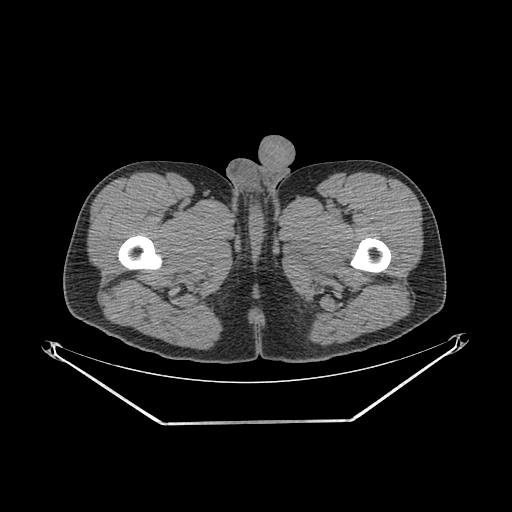
CT of an extremity soft-tissue mass (from a PET/CT study), one axial slice. Slice 266 of 267 in the series (ordered by position). Reconstruction kernel SOFT. Soft-tissue window (W 400 / L 40 HU). 3.75 mm slice thickness. 512 × 512 image matrix, field of view 500 × 500 mm. Male patient. Case-level facts recorded for this patient, not image findings: histological type: extraskeletal osteosarcoma; grade: high; site of the primary tumour: left adductur.
Outlined on this slice (expert contour drawn on MRI and transferred to this co-registered scan by the dataset authors):
- gross tumour volume (mass): bounding box [x1, y1, x2, y2] px = [295, 199, 385, 296]